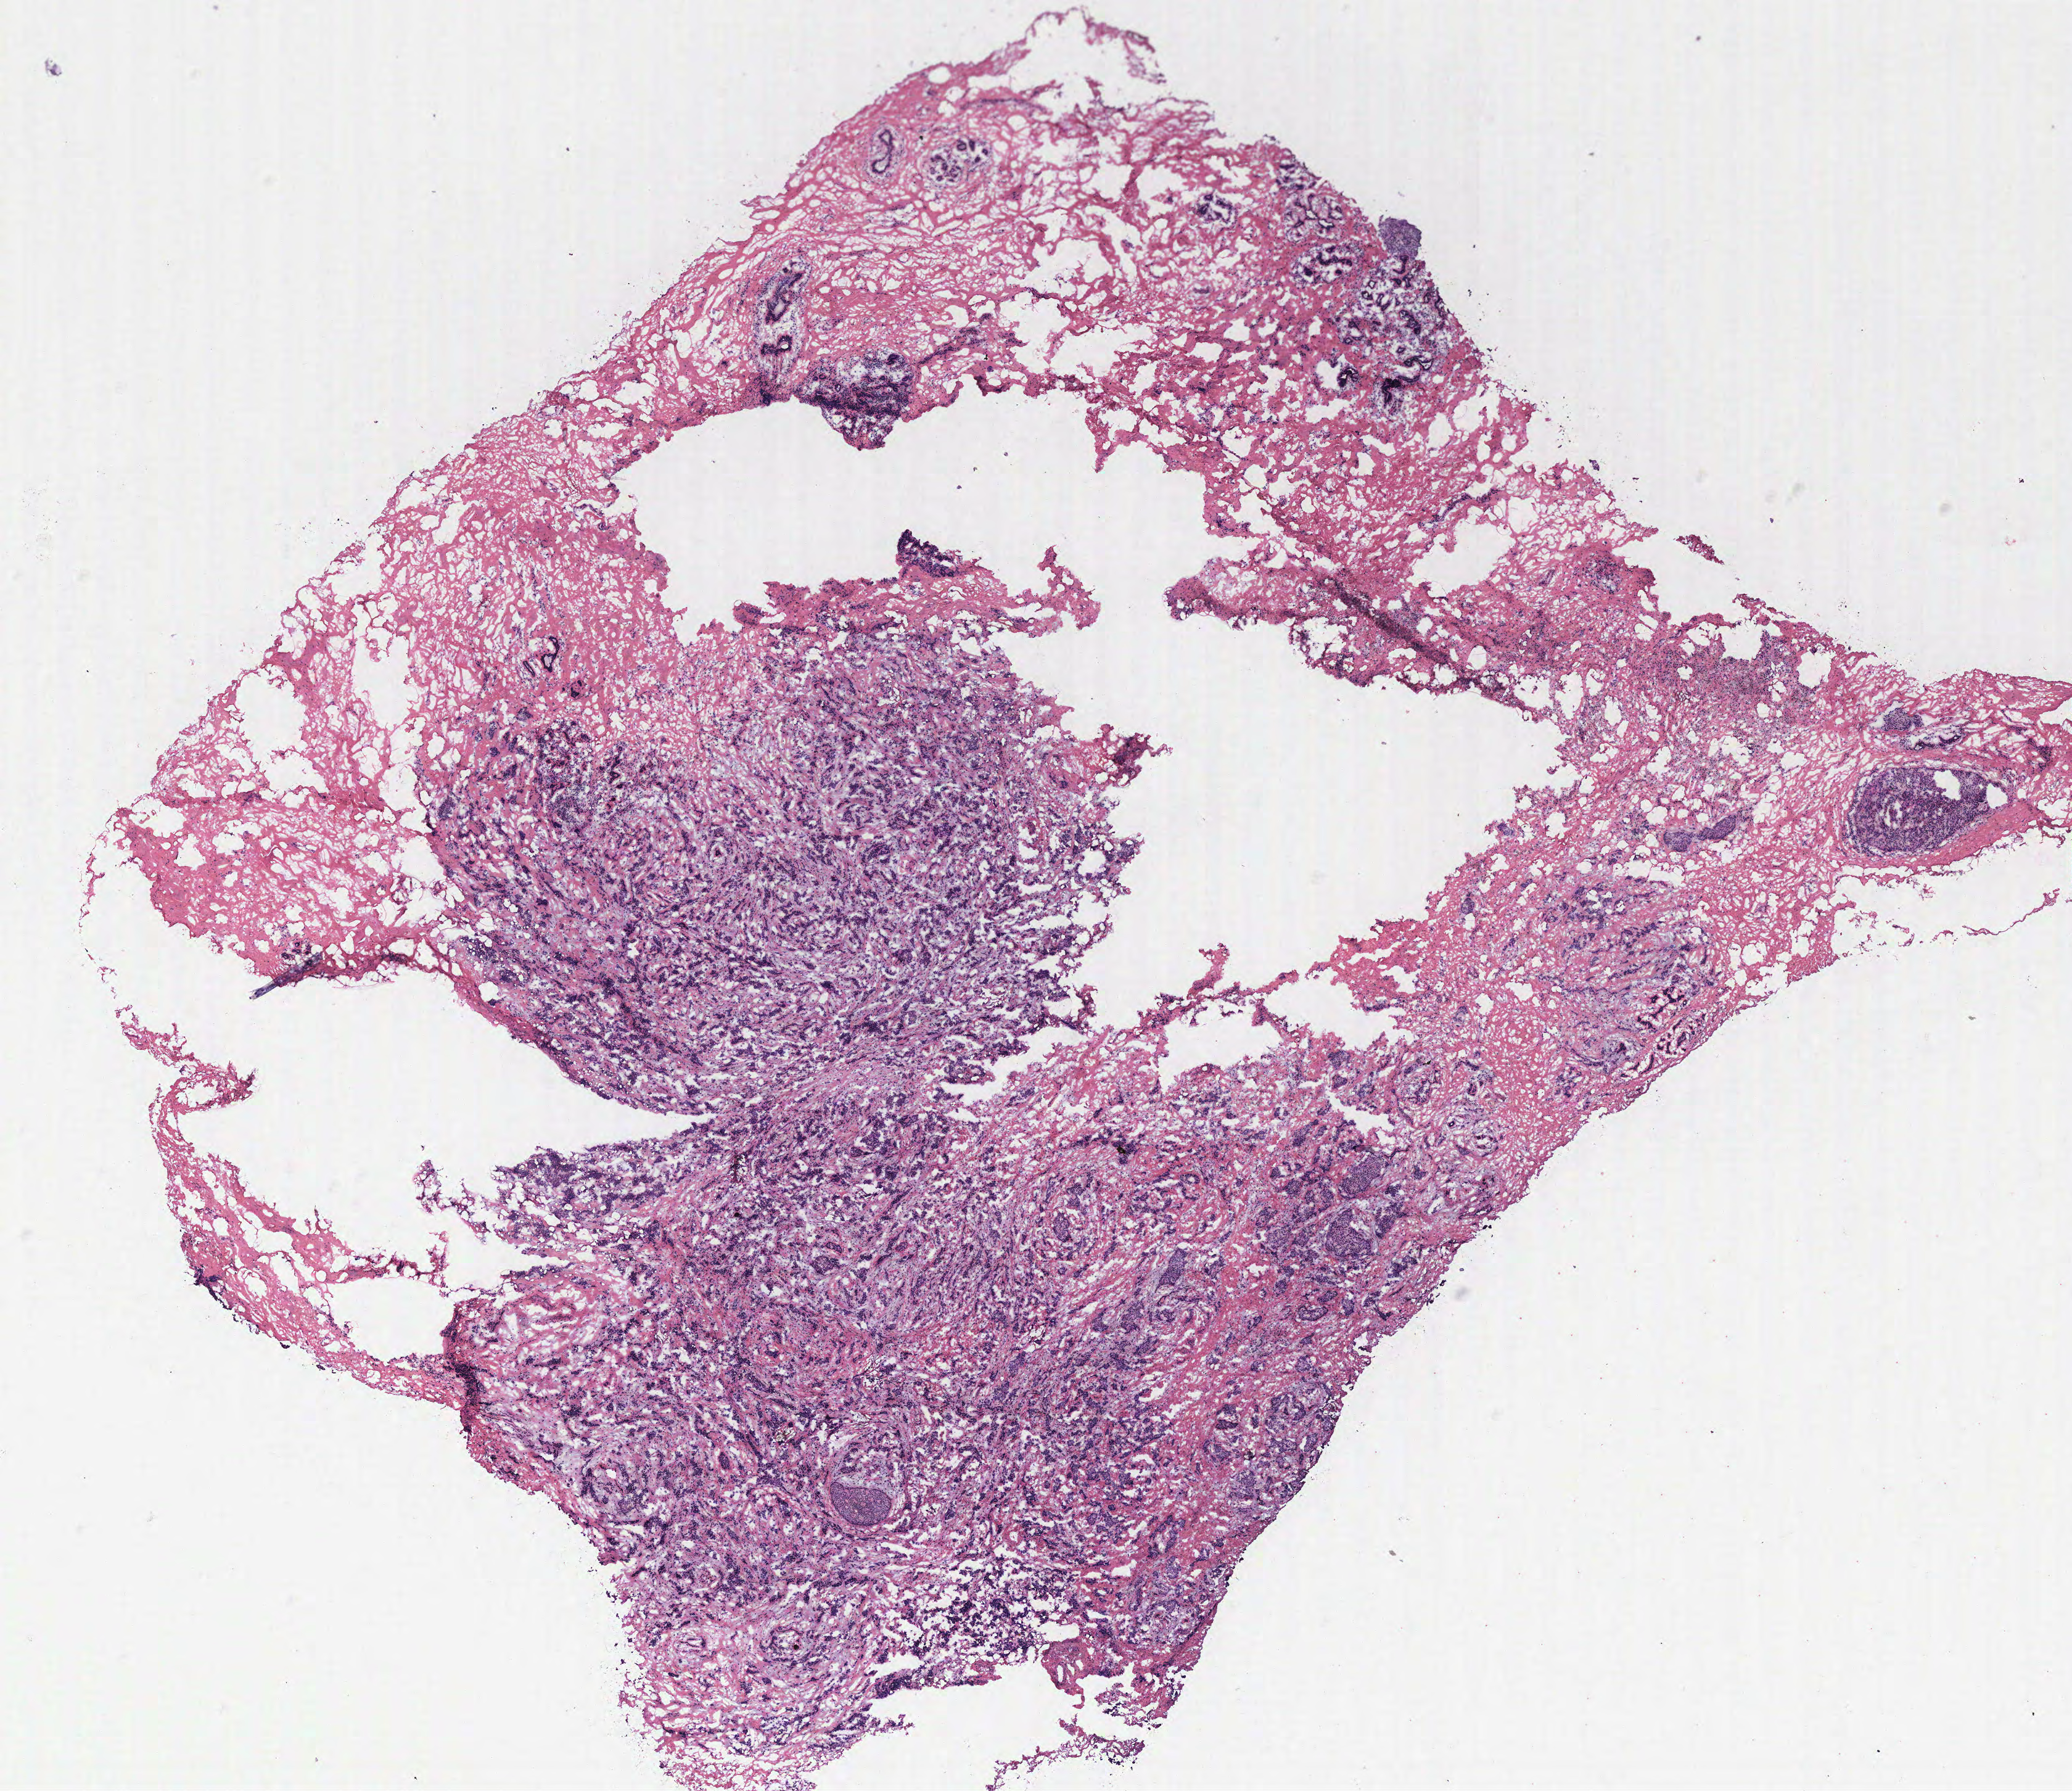
Digitized H&E tissue section (whole slide) — a low-resolution overview of the entire scanned area, about 13.4 x 11.6 mm (from a 40x scan). Tumour tissue sample, breast. Female, 47 y/o.
Histologic diagnosis: Infiltrating duct carcinoma, NOS.